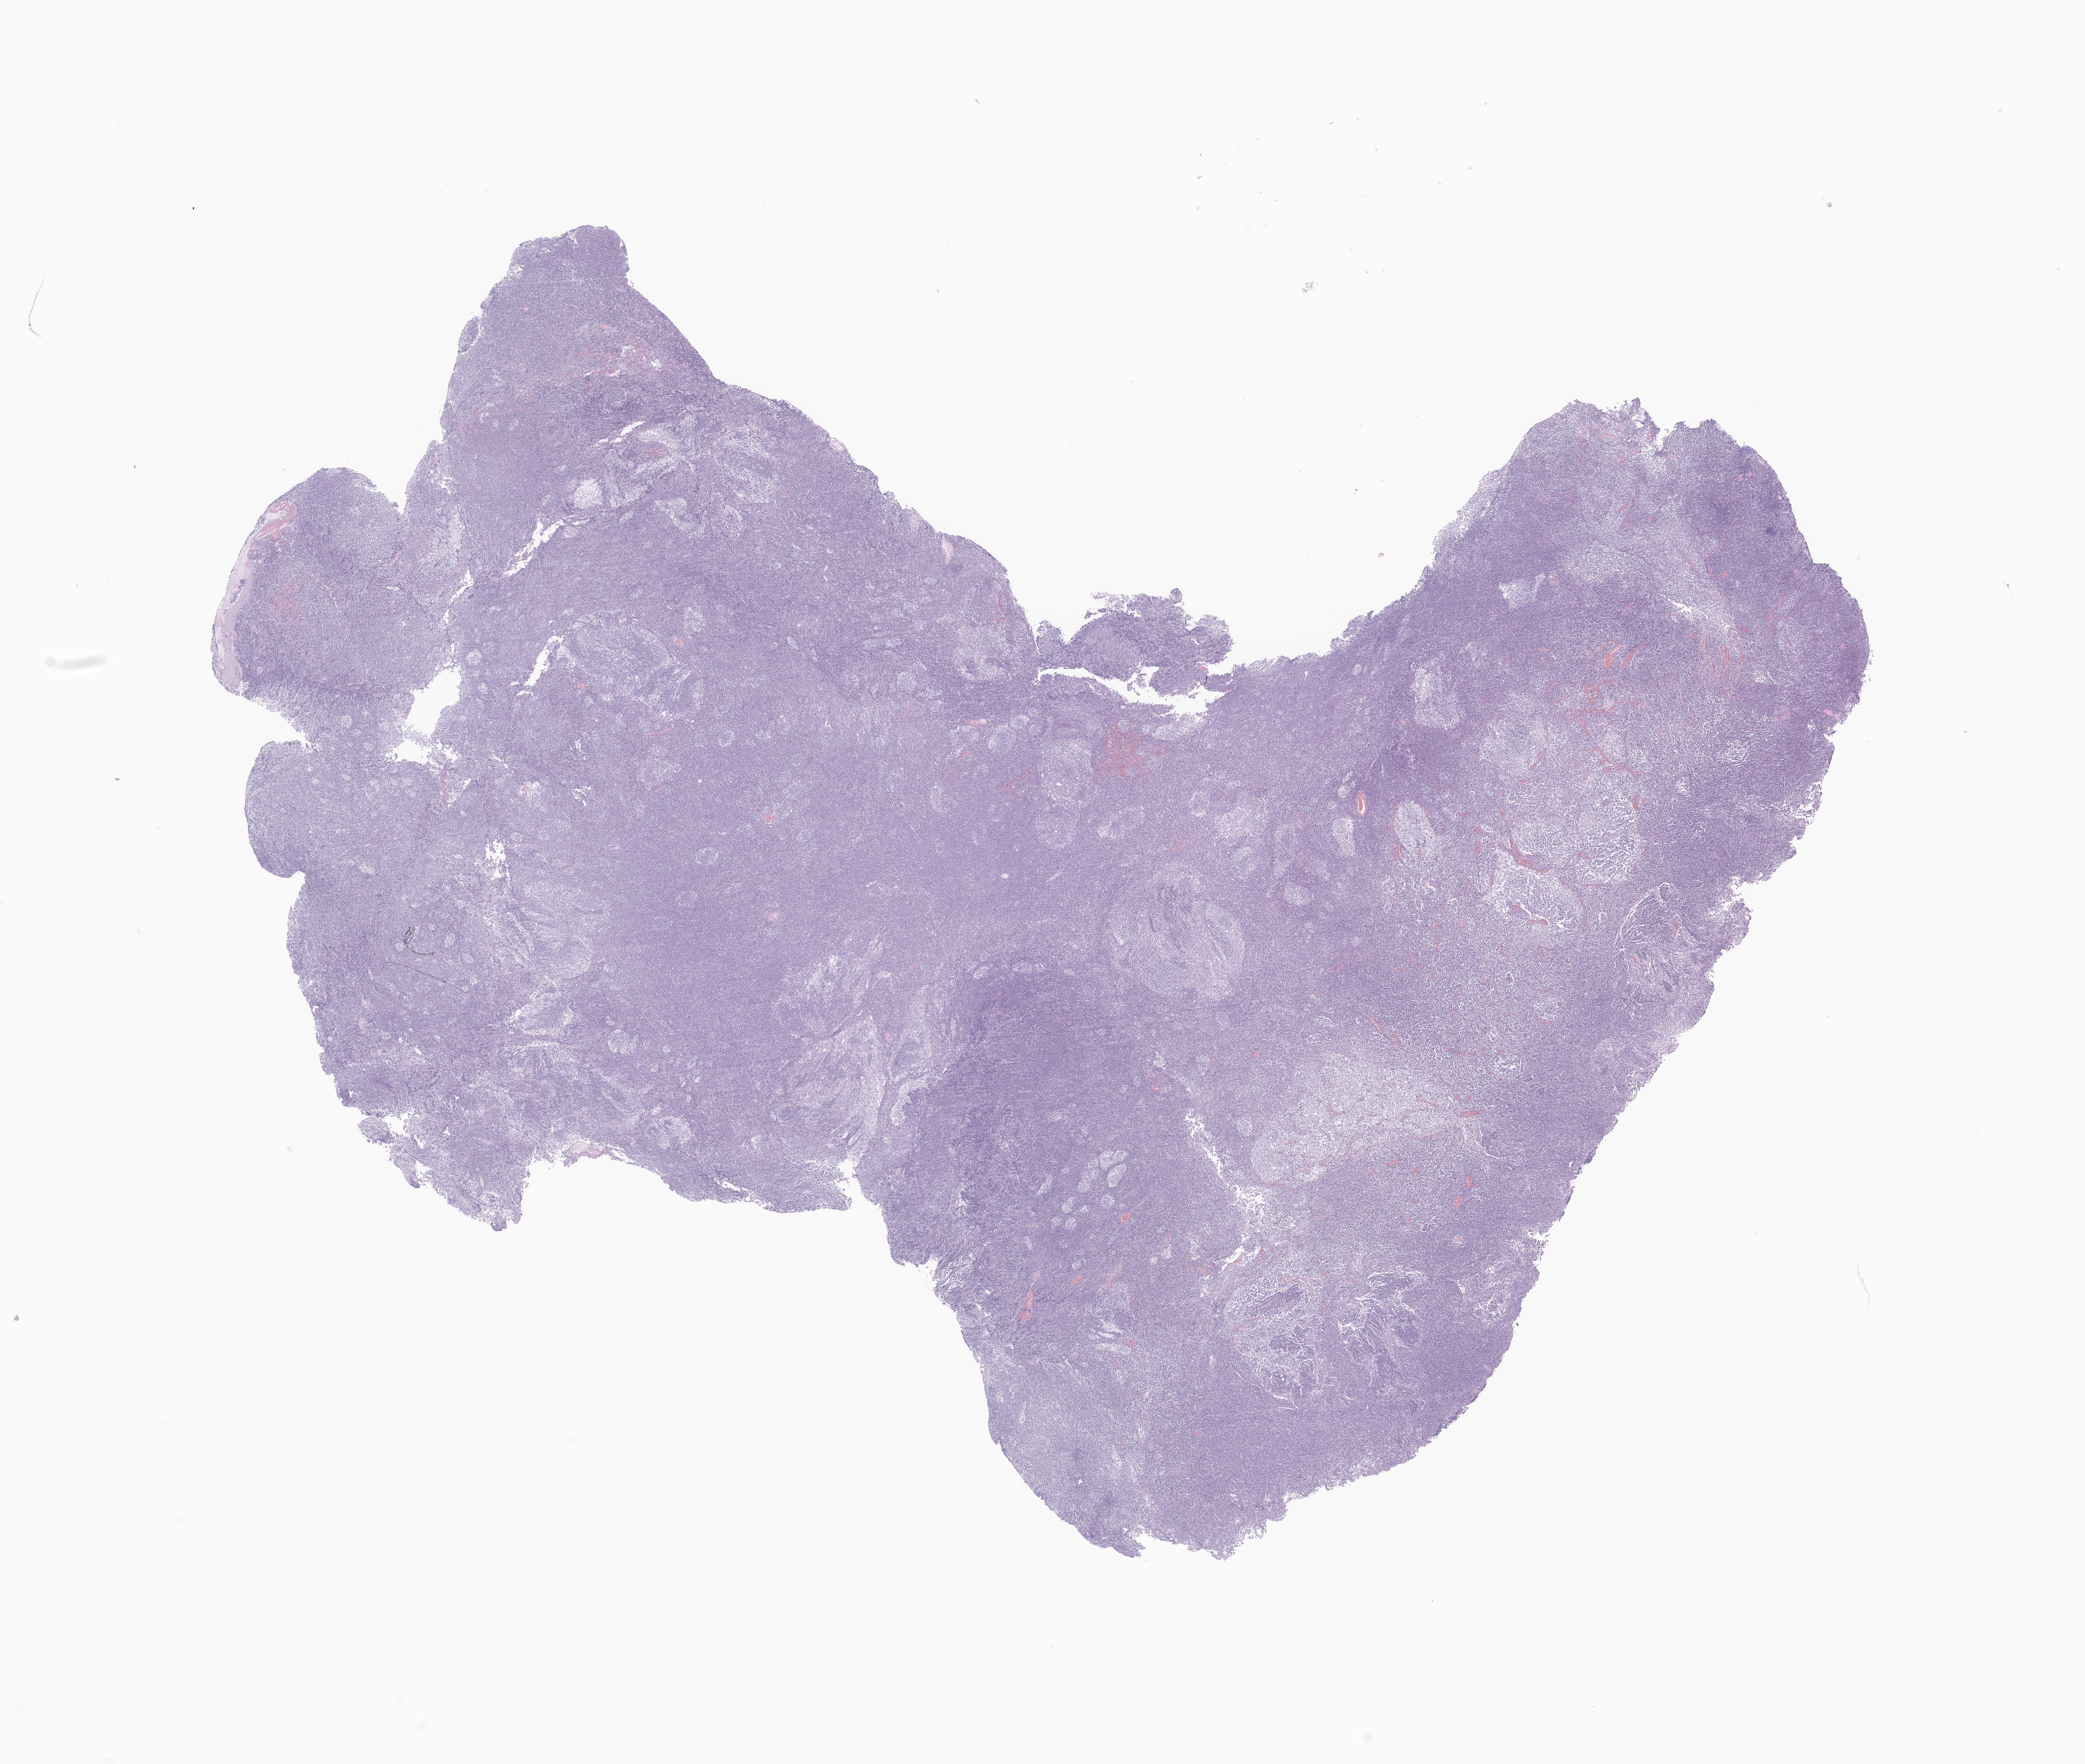
Digitized H&E-stained section of tumor tissue from the cerebellum — whole scanned area (about 18.9 x 16.0 mm) shown as a low-resolution overview, formalin-fixed paraffin-embedded section. Patient: male, age 596 days (about 1.6 years).
- recorded diagnosis: Desmoplastic nodular medulloblastoma